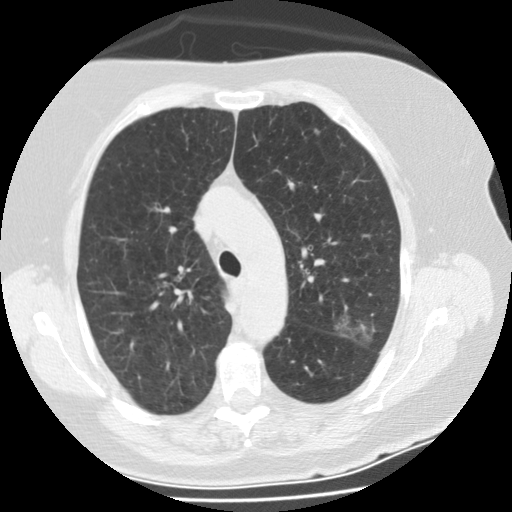
Axial slice from a low-dose chest CT screening exam, second screening round (one year after baseline), lung window (W 1500 / L -600 HU), standard (soft-tissue) reconstruction kernel (STANDARD), 512 × 512 image matrix. Female participant, aged 74 years at enrolment. Former smoker at enrolment.
- Expert-annotated lung lesion, bounding box (x1, y1, x2, y2) in pixels: (326, 306, 386, 360).
- The screening reader recorded 3 non-calcified nodules or masses ≥4 mm on this exam (right lower lobe, left upper lobe, left upper lobe); which of them this box marks is not recorded.
- Participant outcome: lung cancer diagnosed 68 days after this screen — bronchiolo-alveolar adenocarcinoma, NOS, left upper lobe, stage IA (AJCC 6th edition), 20 mm at pathology.